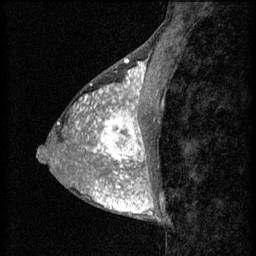
Breast MRI (dynamic contrast-enhanced), one sagittal slice. 3 images stored at this slice position (order not interpretable as contrast timing). 1.5 T. TE 4.2 ms, TR 8.2 ms. 2 mm slice thickness. 256 × 256 image matrix, field of view 180 × 180 mm. Female patient, age 38 years.
Structures marked on this image (semi-automatically segmented with operator editing):
- analysis volume of interest (the breast-tissue region the enhancement analysis was run in; not a lesion): box from (x=95, y=106) to (x=157, y=171) px
- tumour enhancement mask (voxels above the 70 % enhancement threshold inside the analysis volume of interest): (x=95, y=106)–(x=148, y=171)